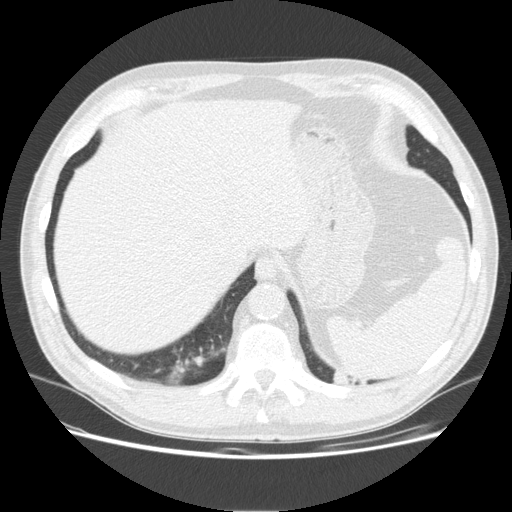
Low-dose screening chest CT, one axial slice. Reconstruction kernel STANDARD. 120 kVp. Lung window (W 1500 / L -600 HU). 2.5 mm slice thickness. 512 × 512 image matrix.
Outlined on this slice (manually delineated by an expert):
- lesion 1 (tumor, upper lobe of left lung): box from (x=333, y=371) to (x=369, y=384) px